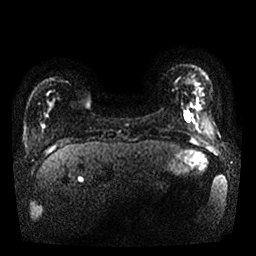
Breast MRI, one axial slice. Diffusion-weighted series; image 2 of 4 stored at this slice position (different b-values; order by instance number). 1.5 T. 4 mm slice thickness. 256 × 256 image matrix, field of view 340 × 340 mm. Female patient.
Outlined on this slice (manually delineated by an expert):
- tumour on diffusion-weighted imaging: box from (x=184, y=113) to (x=193, y=122) px